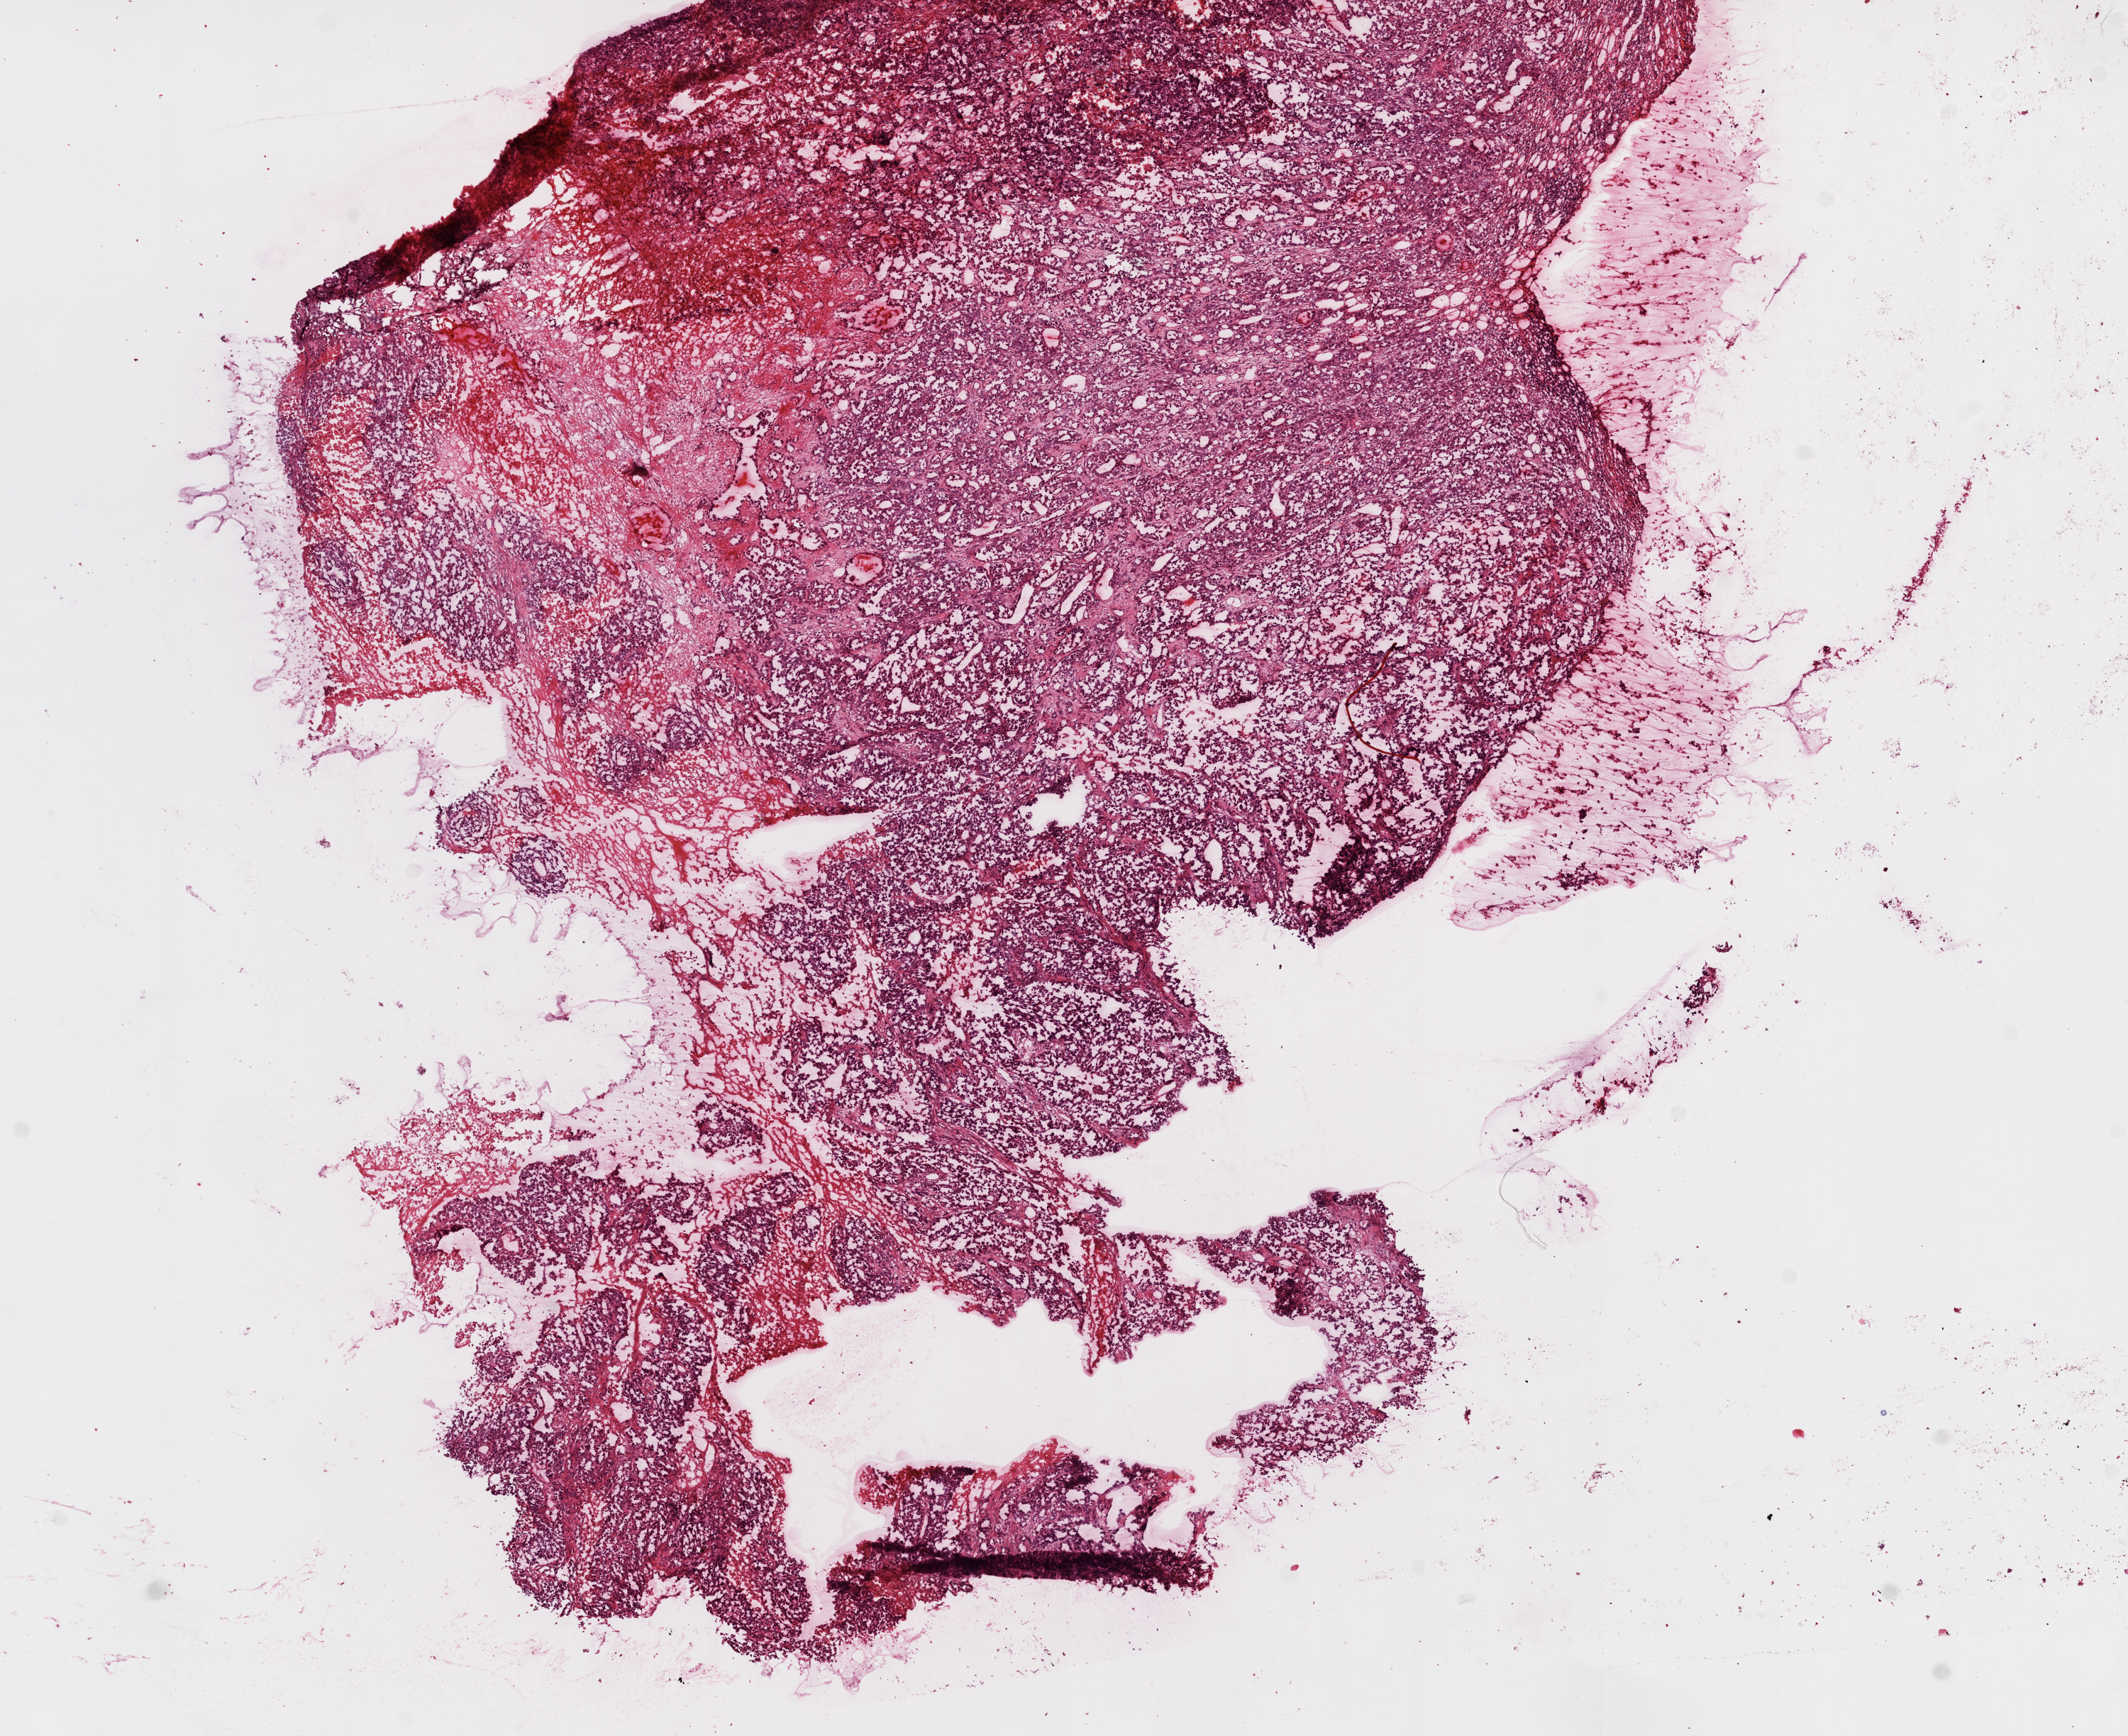
Whole-slide histology image, H&E-stained — a low-resolution overview of the entire scanned area, about 12.0 x 9.8 mm (from a 20x scan), frozen section, kidney, primary tumour sample. Female patient; age at initial diagnosis 53 years. Histologic grade: G3 (poorly differentiated). Composition of this section per pathologist review: tumour cells 75%, tumour nuclei 85%, normal cells 0%, stromal cells 10%, necrosis 15%.
Laterality: right. Histologic diagnosis: Clear cell adenocarcinoma, NOS. AJCC pathologic stage: I.